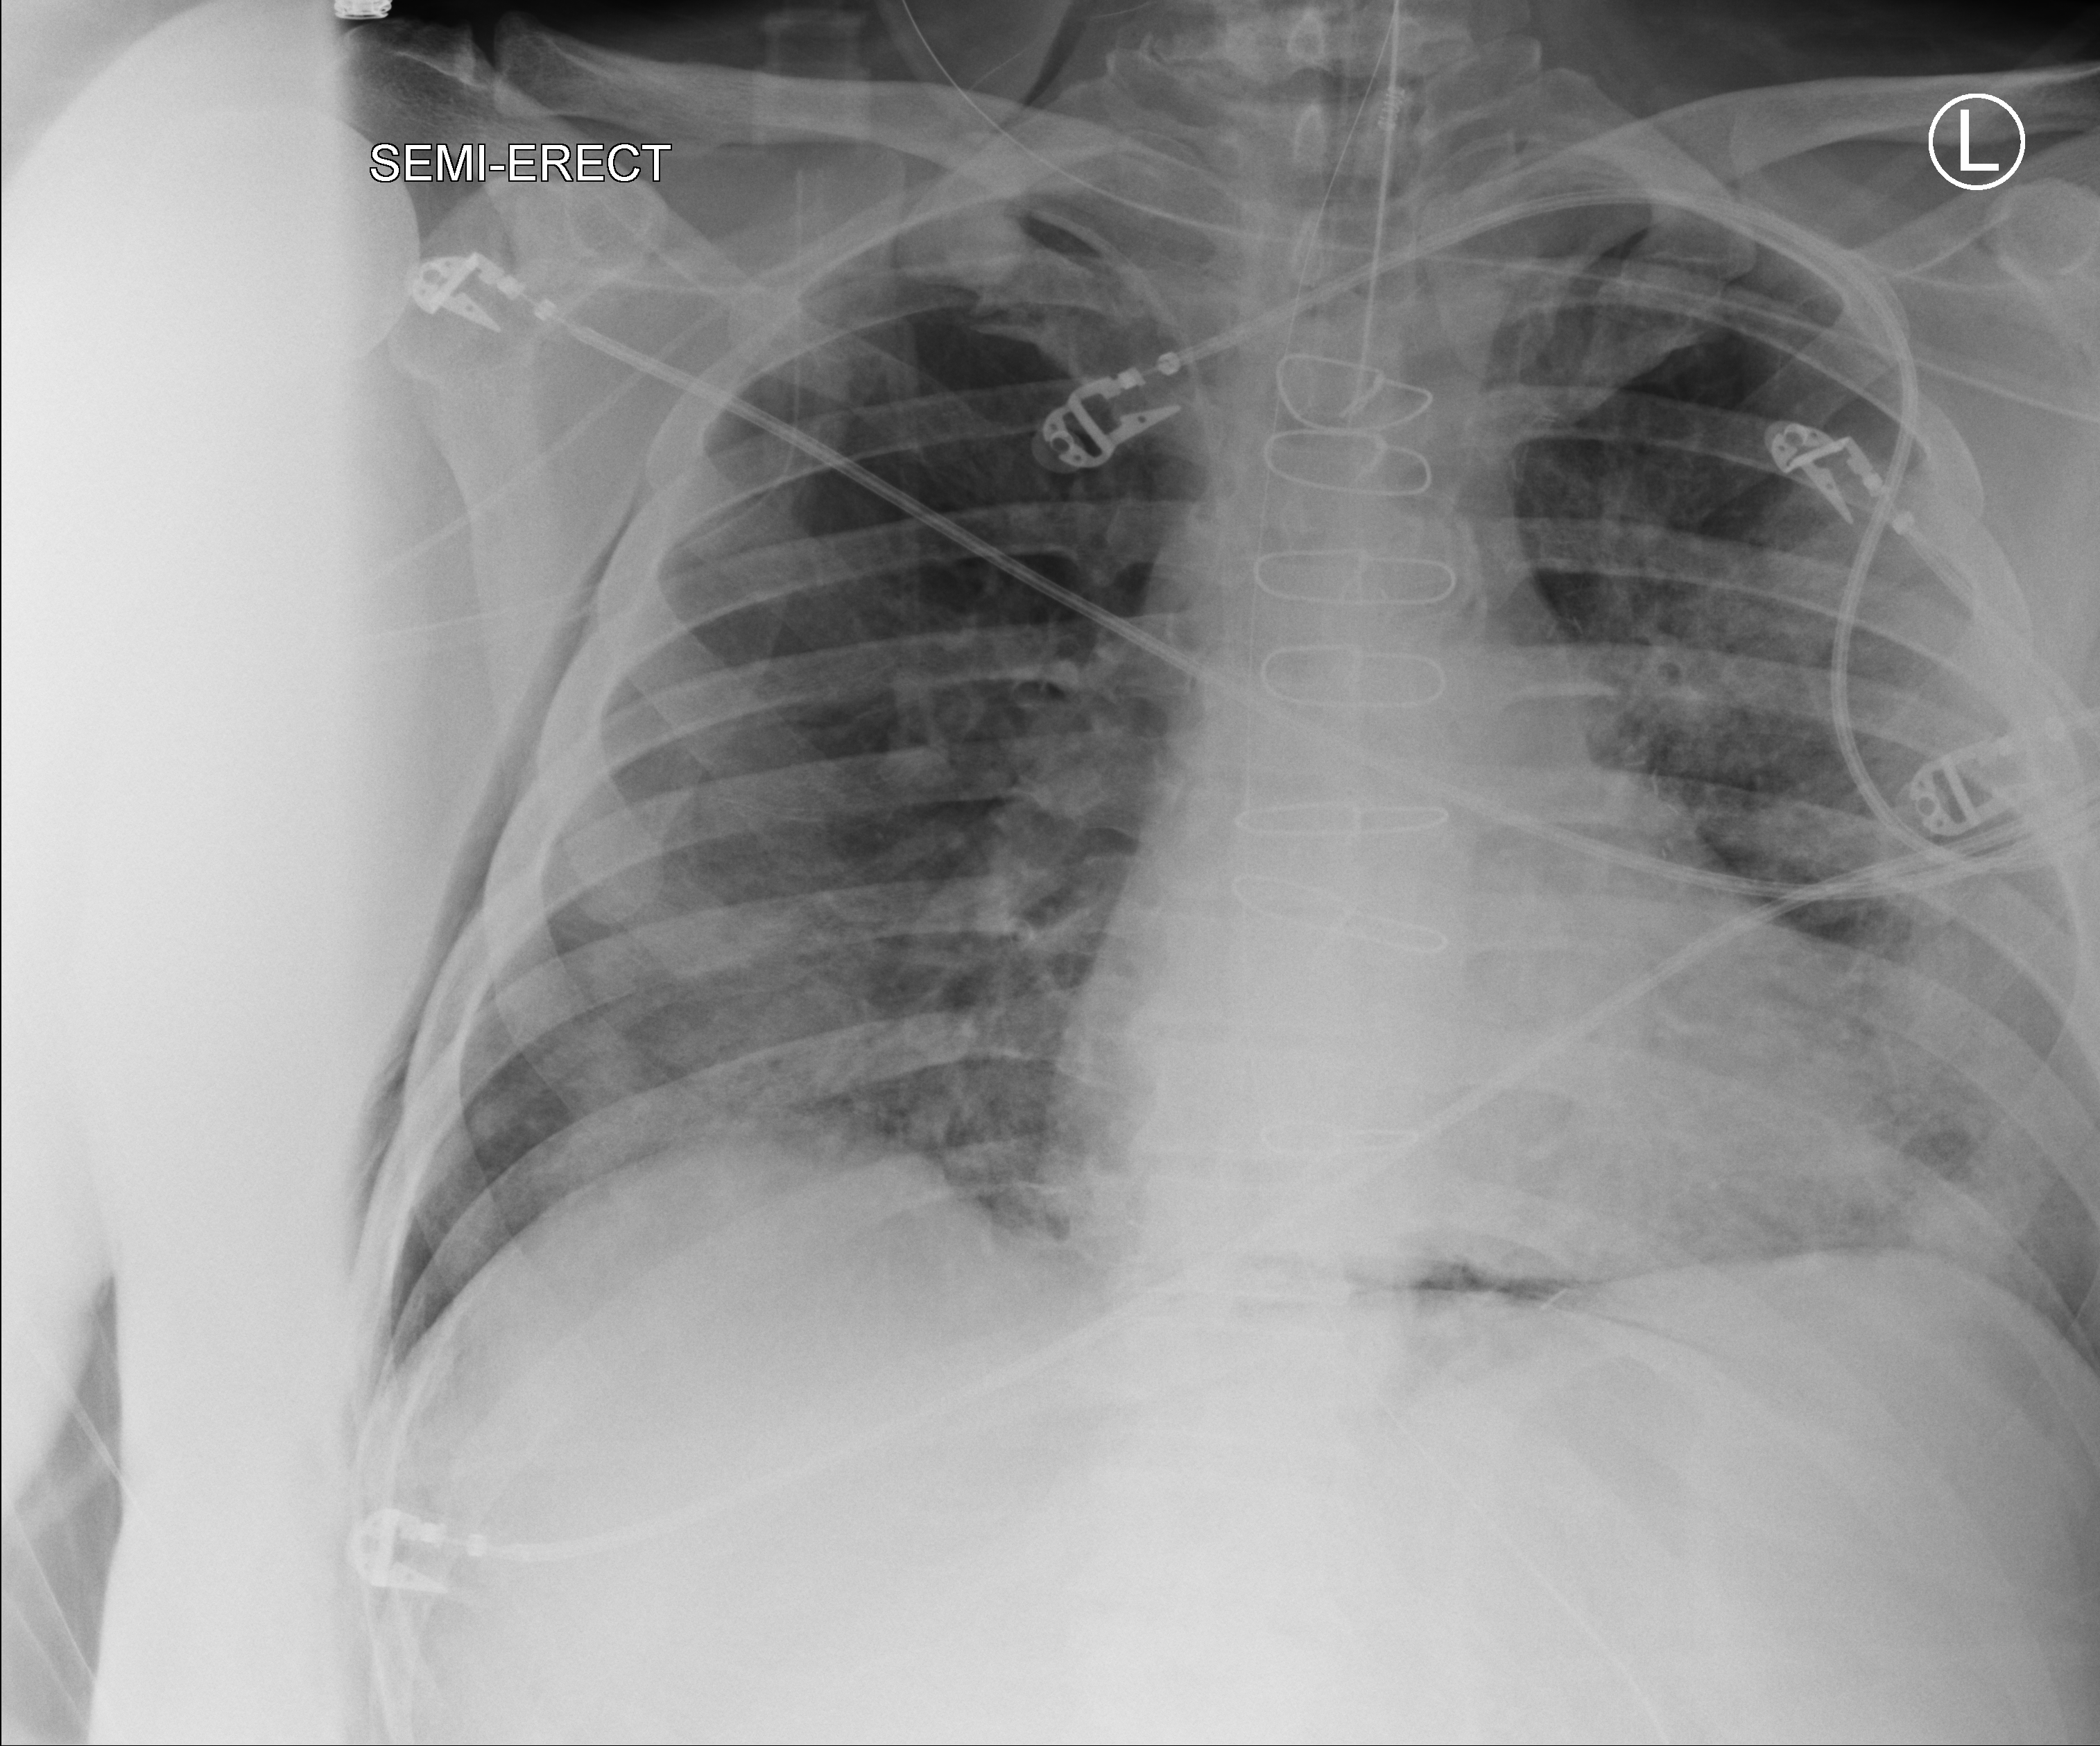
Chest X-ray (portable), anteroposterior (AP) projection. Patient hospitalised with COVID-19; male, aged 60–74 years.
Admission-level facts for this patient (not findings on this image; timing relative to this image not recorded): mechanically ventilated during this hospital stay: yes; admitted to intensive care during this hospital stay: yes; COPD (admission record): no.